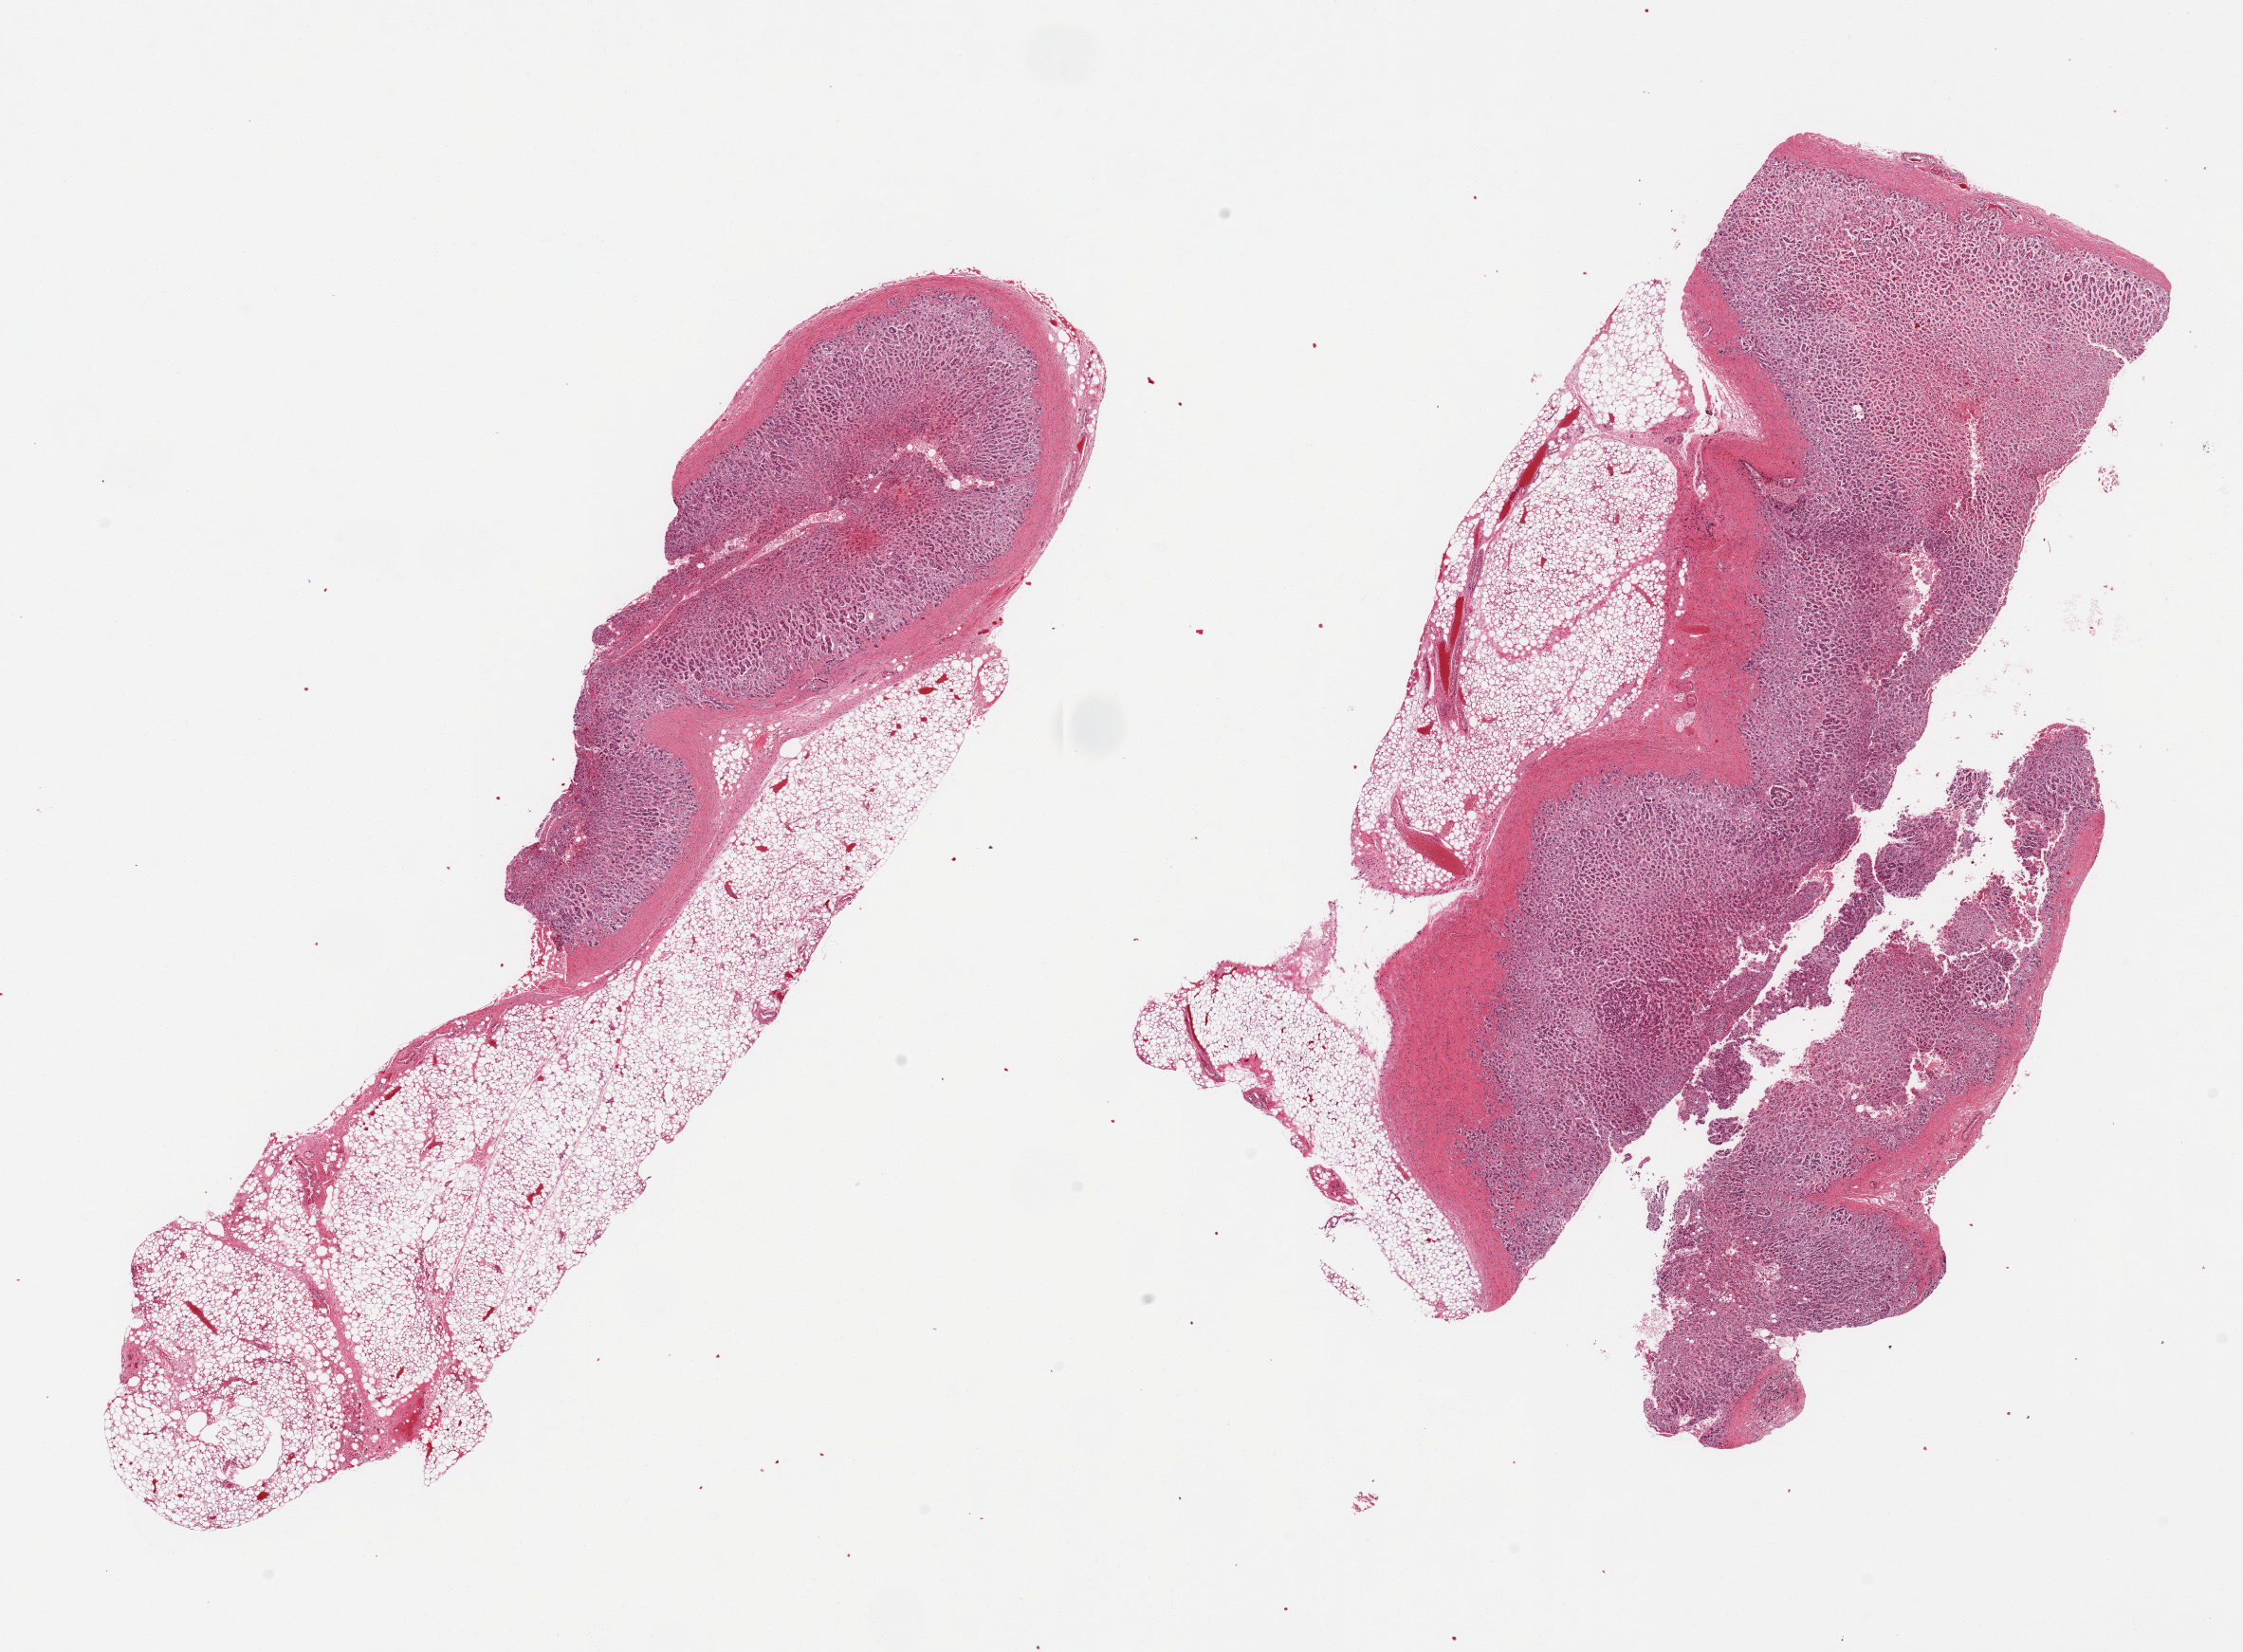
Hematoxylin and eosin (H&E) whole-slide image — whole scanned area (about 18.7 x 13.8 mm) shown as a low-resolution overview. PAXgene-fixed paraffin-embedded (PFPE) section. Target tissue: adrenal gland. Donor tissue sample.
Reviewer comment on this tissue sample: 2 pieces; 50% & 40% external fat content.